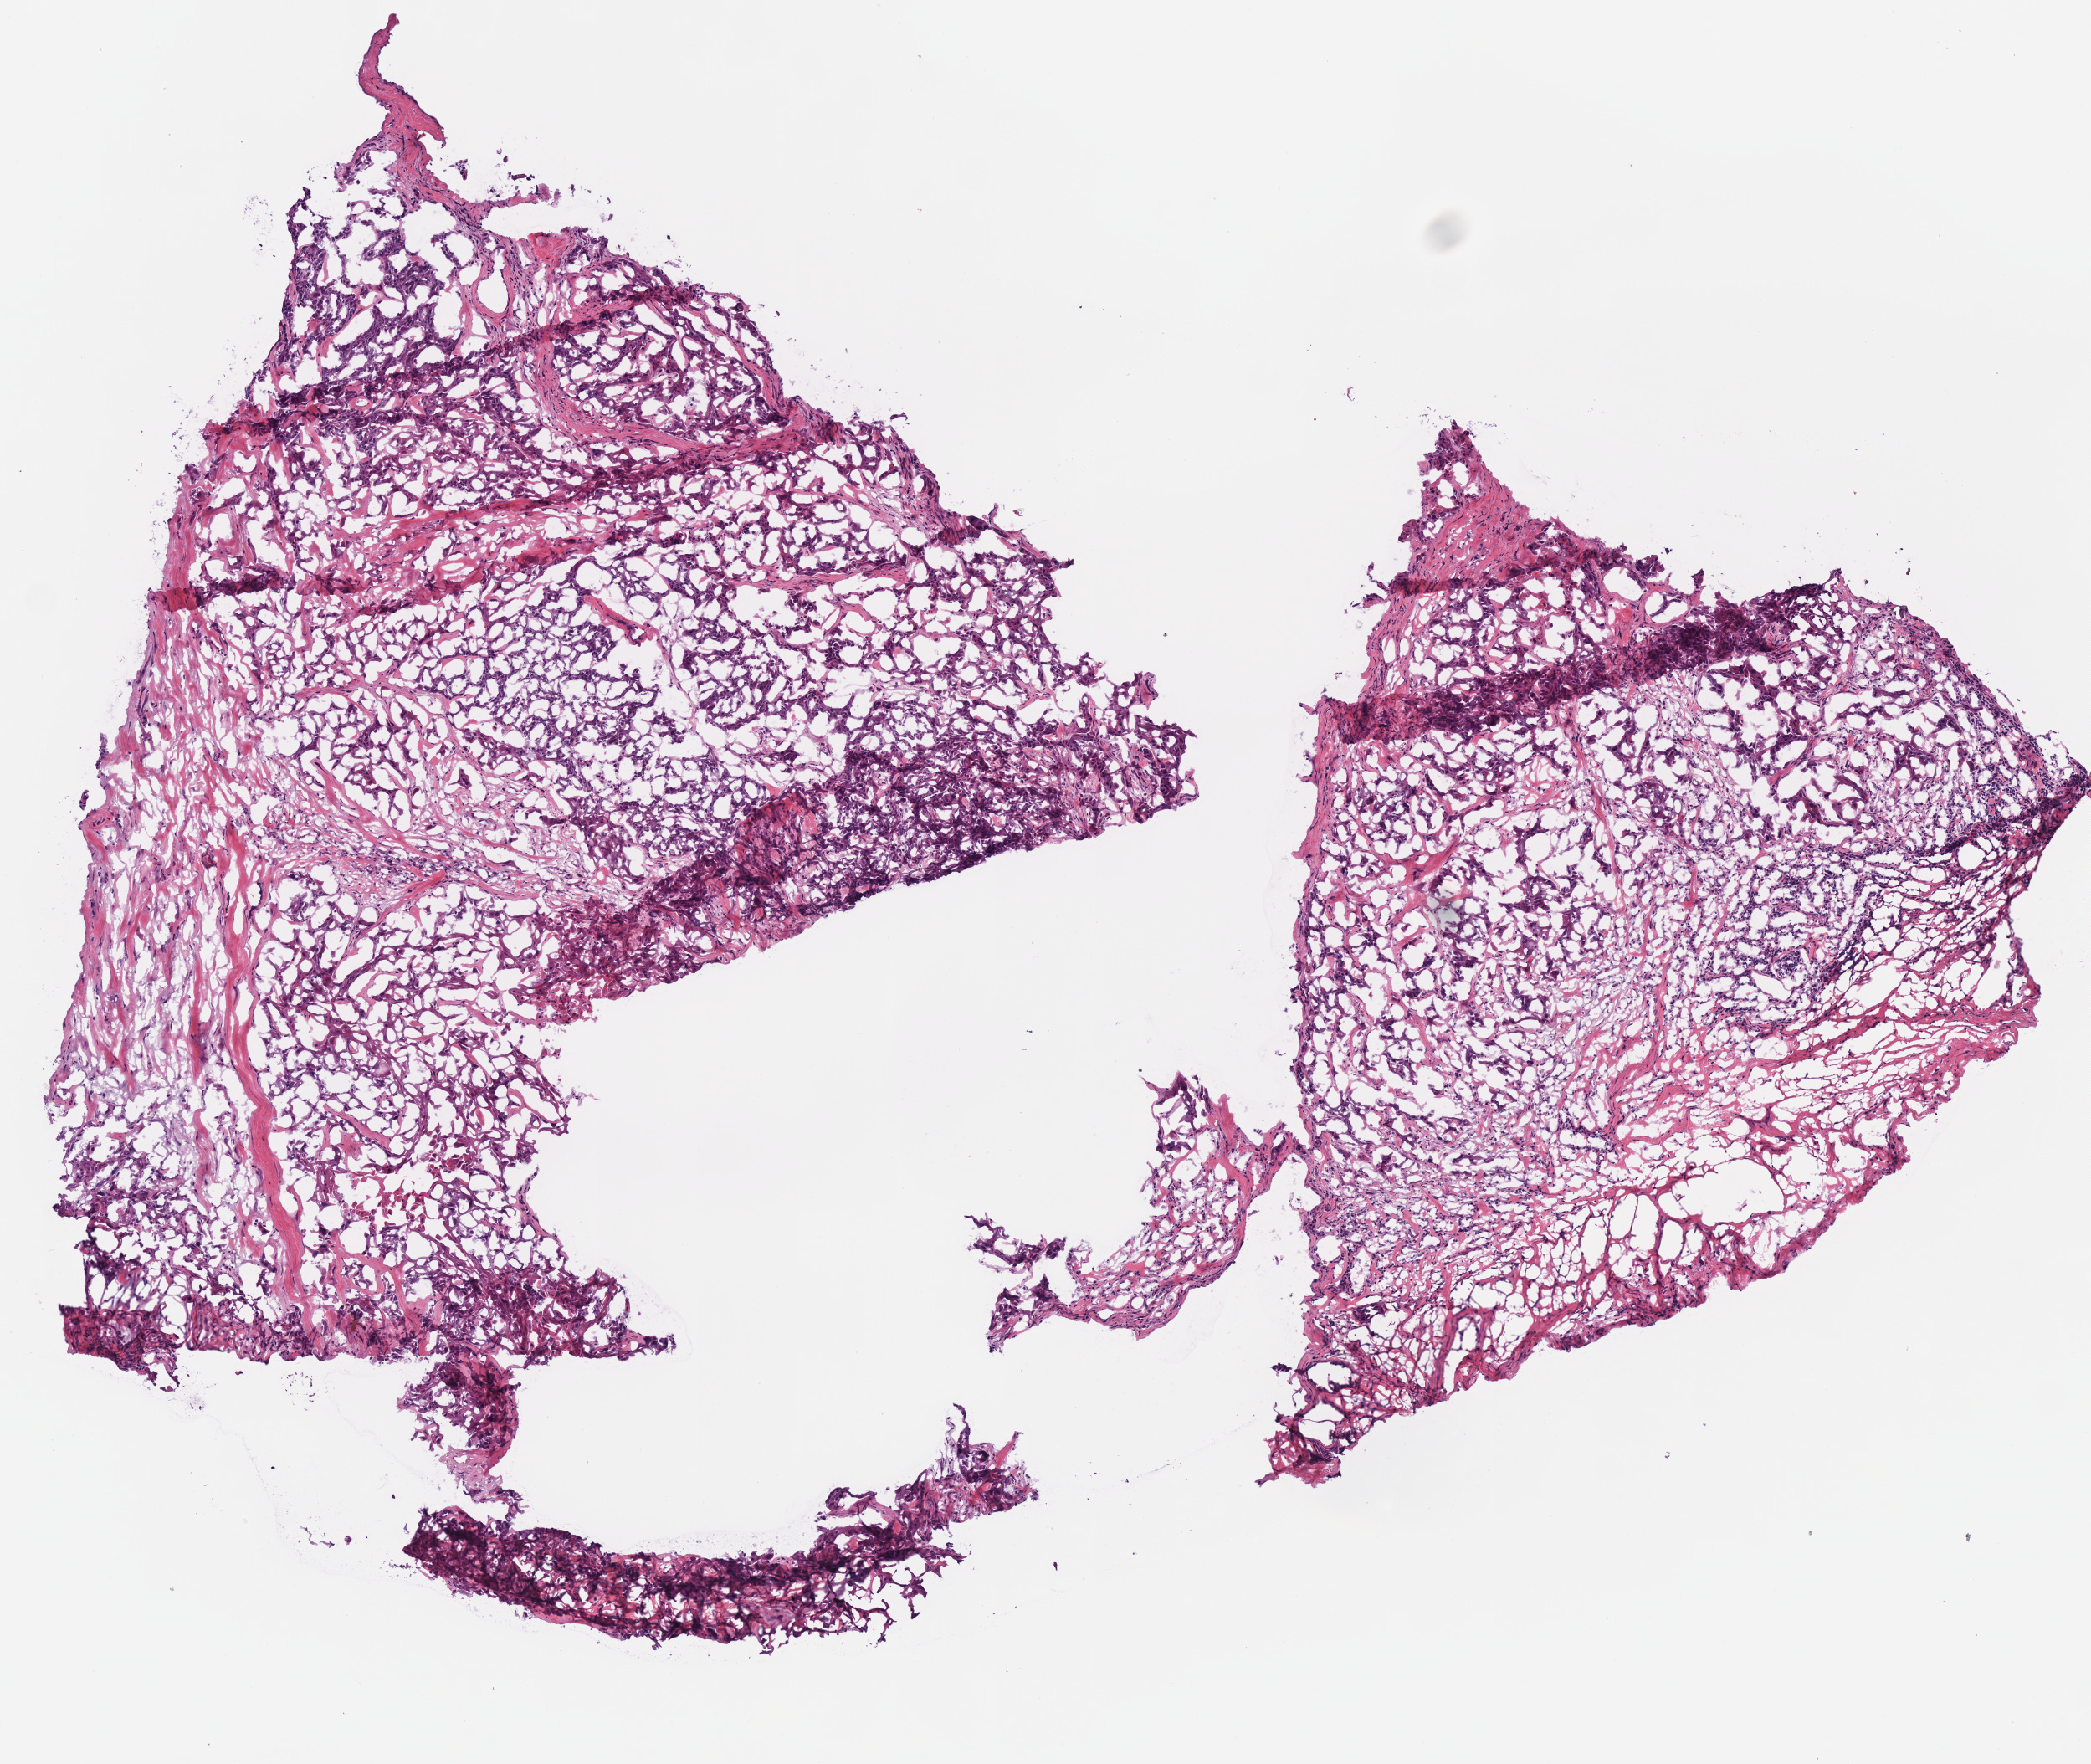
H&E whole-slide image — whole scanned area (about 4.9 x 4.2 mm, acquisition: 40x scan) shown as a low-resolution overview. Frozen section. Head and neck, primary tumour sample. Patient: male, age at initial diagnosis 77 years.
Pathologic diagnosis: Squamous cell carcinoma, NOS.